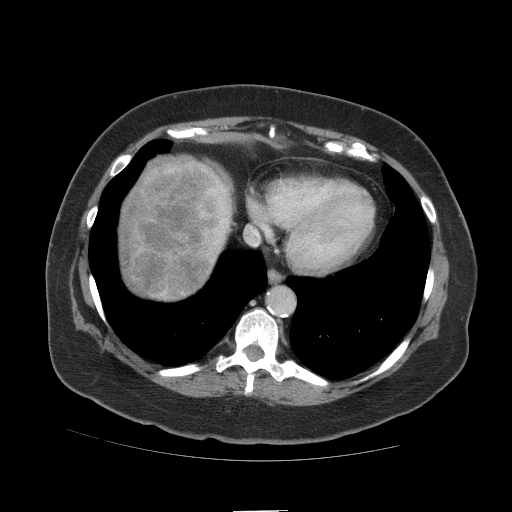
Contrast-enhanced abdominal CT (liver protocol), one axial slice; reconstruction kernel STANDARD; 140 kVp; soft-tissue window (W 400 / L 40 HU); 512 × 512 image matrix, field of view 420 × 420 mm. From the clinical record (not read from this slice): diagnosis: hepatocellular carcinoma (patient treated with transarterial chemoembolisation; whether this scan precedes or follows treatment is not stated here); TNM stage (as recorded): Stage-IVB.
Annotated regions visible in this slice (semi-automatic segmentation, software-assisted and operator-edited):
- liver parenchyma outside the tumour (the mass and vessels are separate outlines, so this box may not span the whole liver): bounding box (x1, y1, x2, y2) in pixels: (120, 156, 232, 300)
- mass: (121, 160, 230, 295)